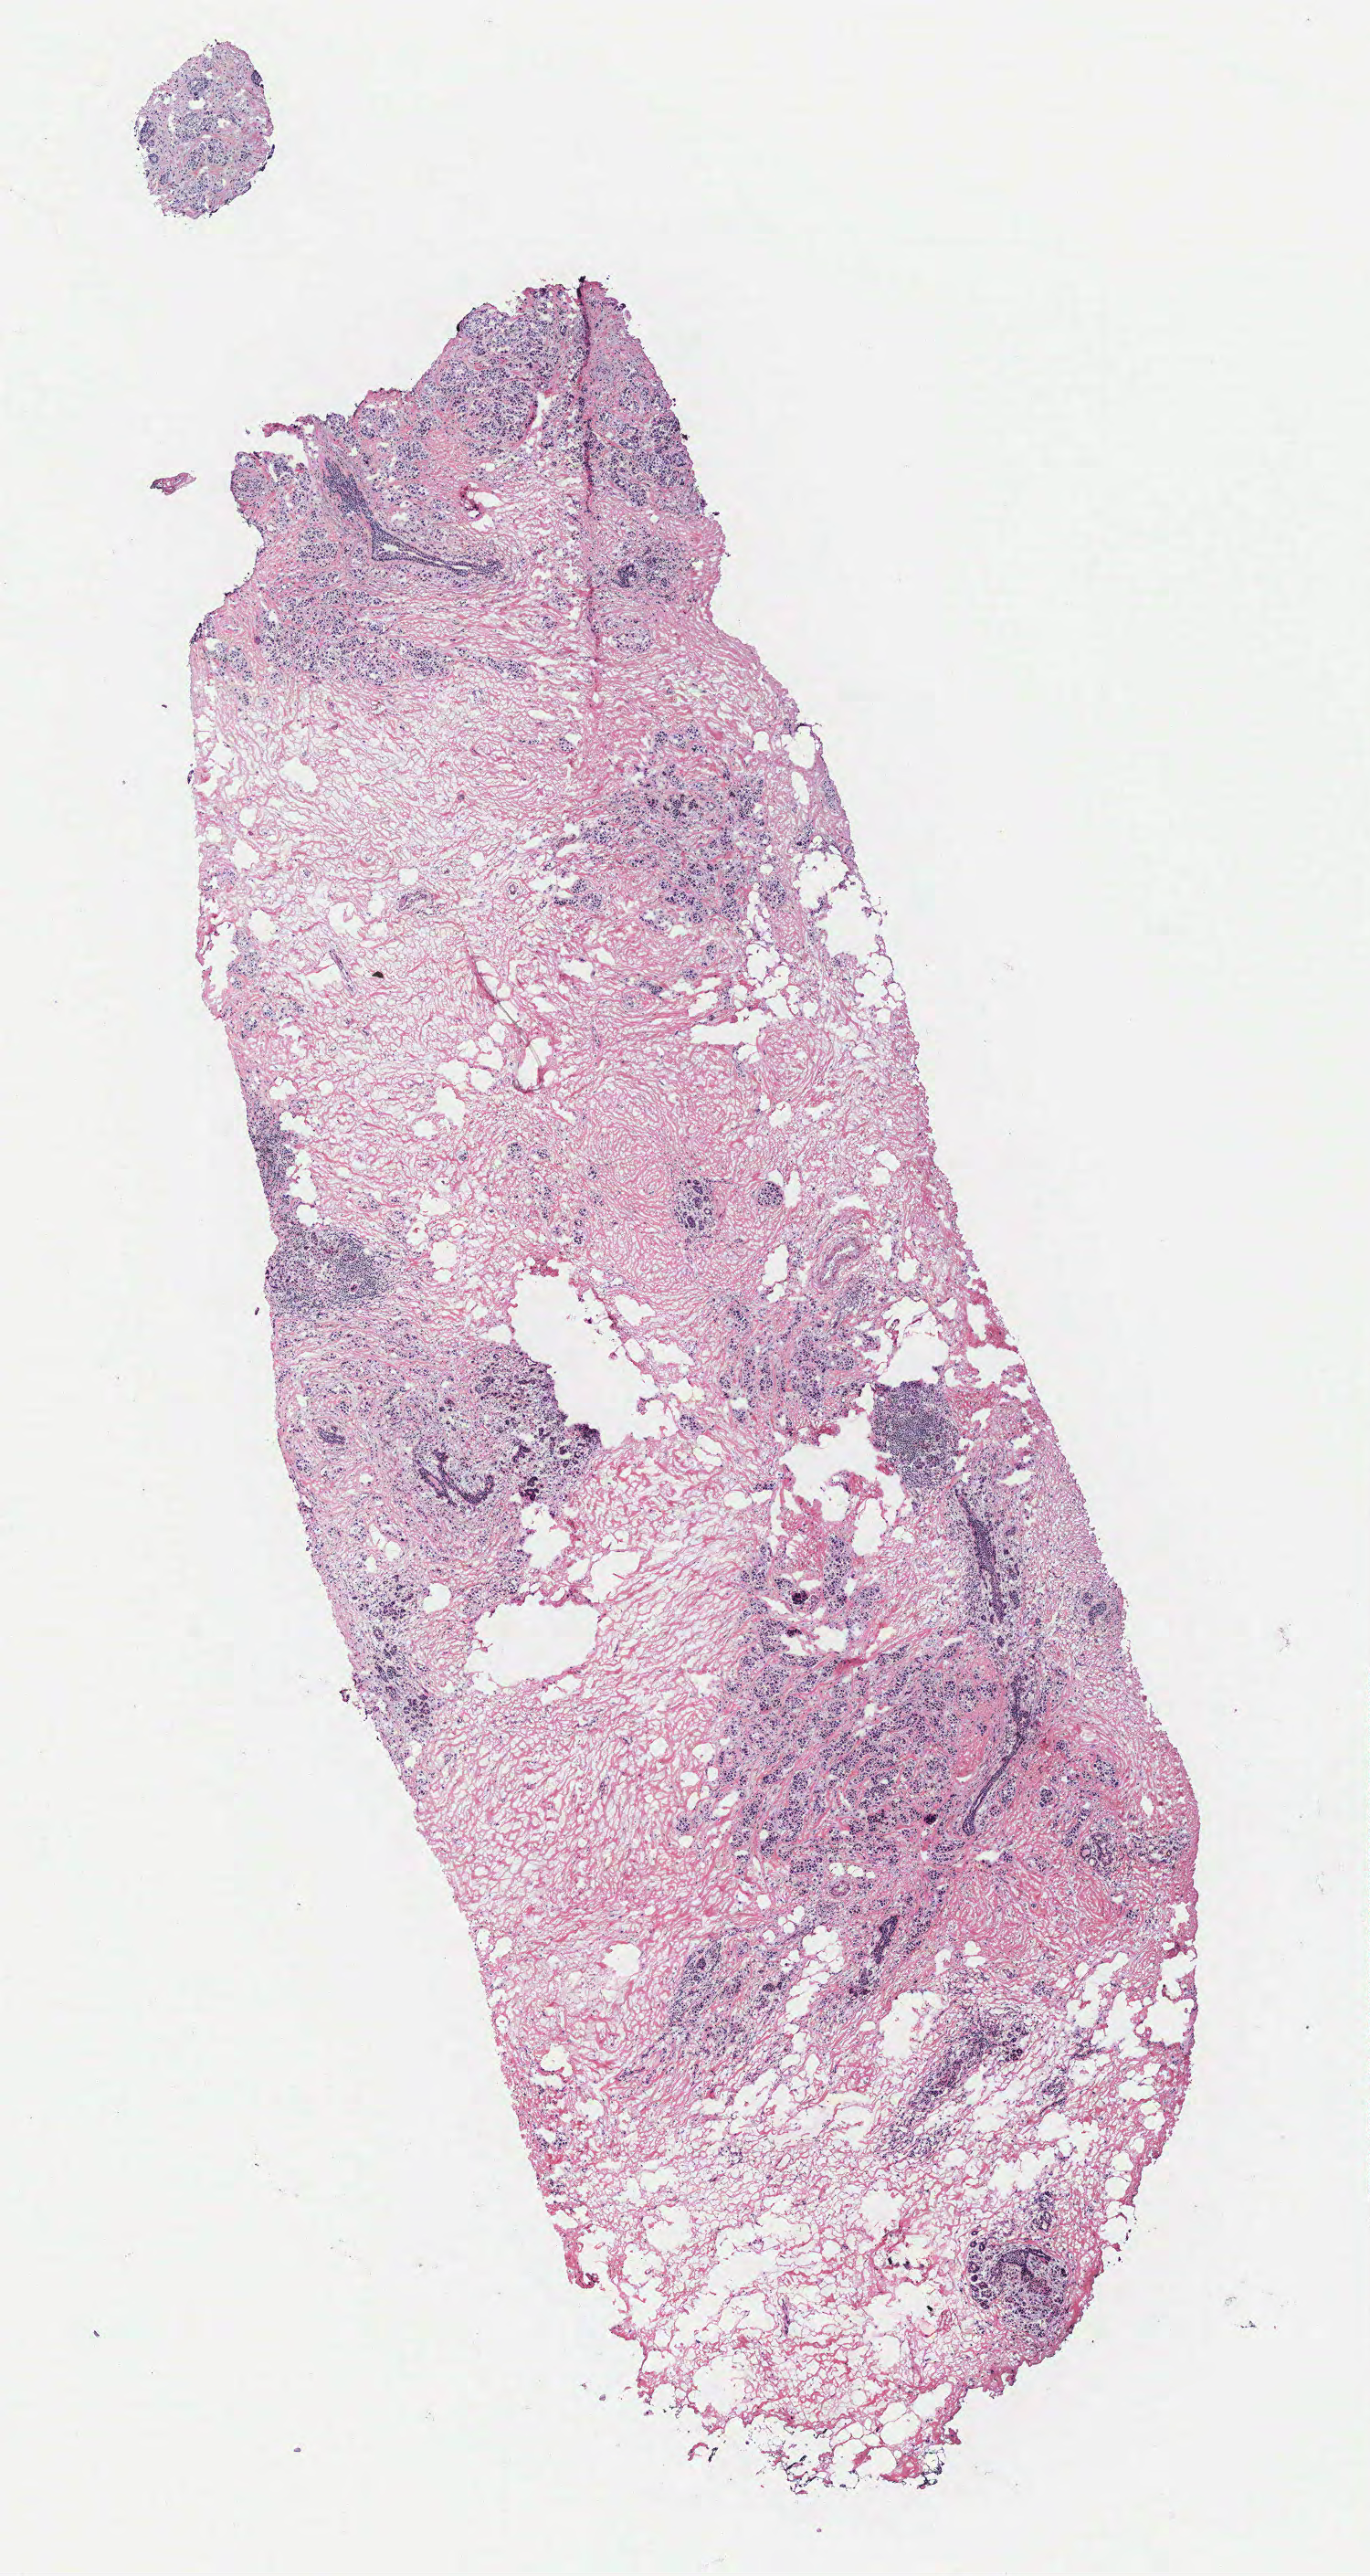
Hematoxylin and eosin (H&E) stained whole-slide image, whole scanned area (about 6.0 x 11.3 mm, from a 40x scan) shown as a low-resolution overview; breast, tissue type not recorded.
Patient diagnosis (cohort enrolment): breast cancer (breast).